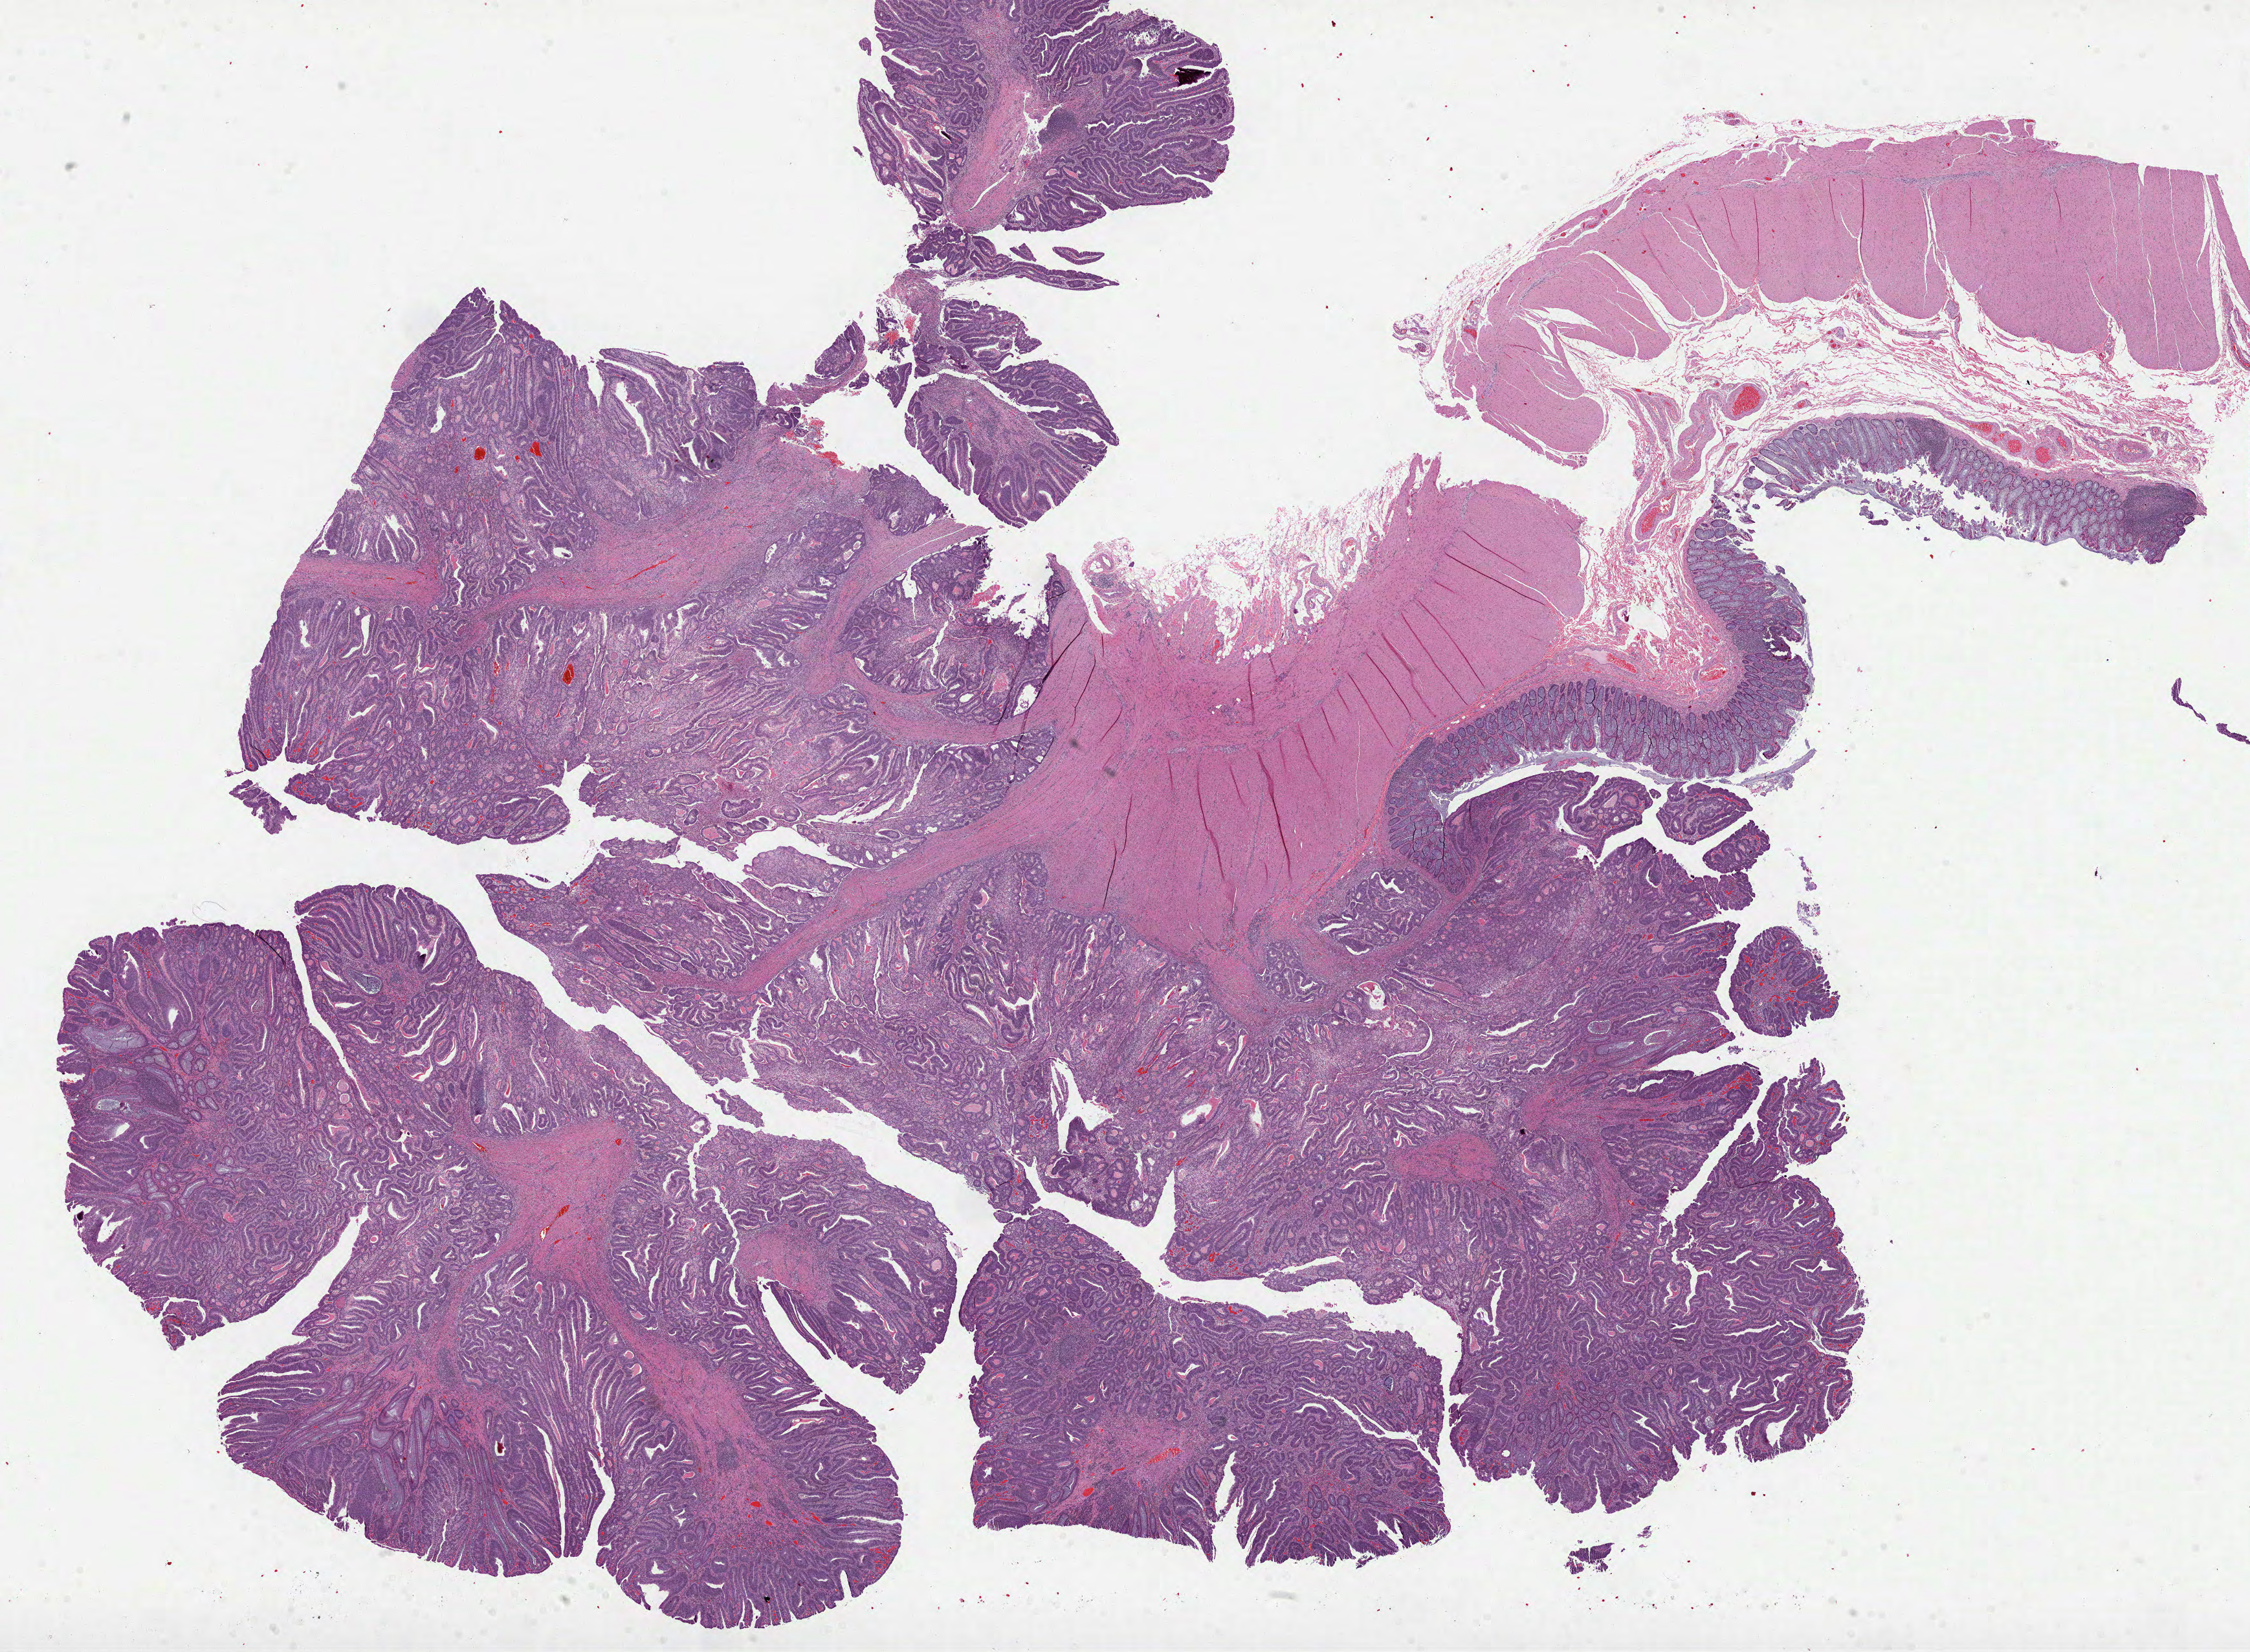
Digitized H&E tissue section (whole slide) — a low-resolution overview of the entire scanned area, about 28.0 x 20.6 mm (from a 40x scan), formalin-fixed paraffin-embedded (FFPE) diagnostic section, sample: primary tumour, colon. Patient: female, age at initial diagnosis 36 years.
AJCC pathologic stage: I. Lymph nodes positive (case pathology): 0 of 31 examined. TNM: T2 N0 M0. Pathologic diagnosis: Adenocarcinoma, NOS.